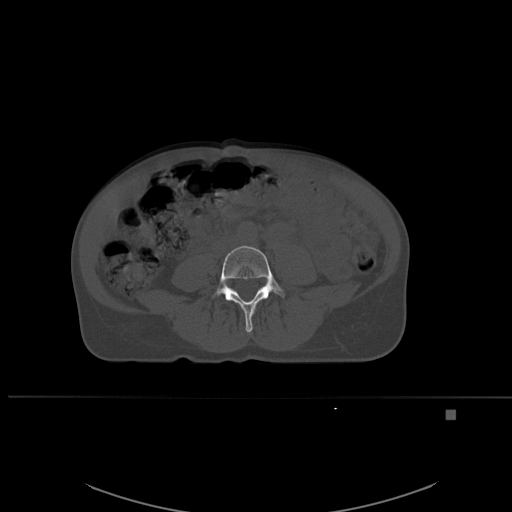
CT including the spine, one axial slice. Slice 191 of 537 in the series (ordered by position). Bone window (W 1800 / L 400 HU). 1.5 mm slice thickness. 512 × 512 image matrix, field of view 440 × 440 mm. Patient: female, 45 years. From the clinical record (not read from this slice): primary cancer: lung.
Outlined on this slice (semi-automatically segmented with operator editing):
- L4 vertebra: bounding box (x1, y1, x2, y2) in pixels: (213, 245, 285, 333)